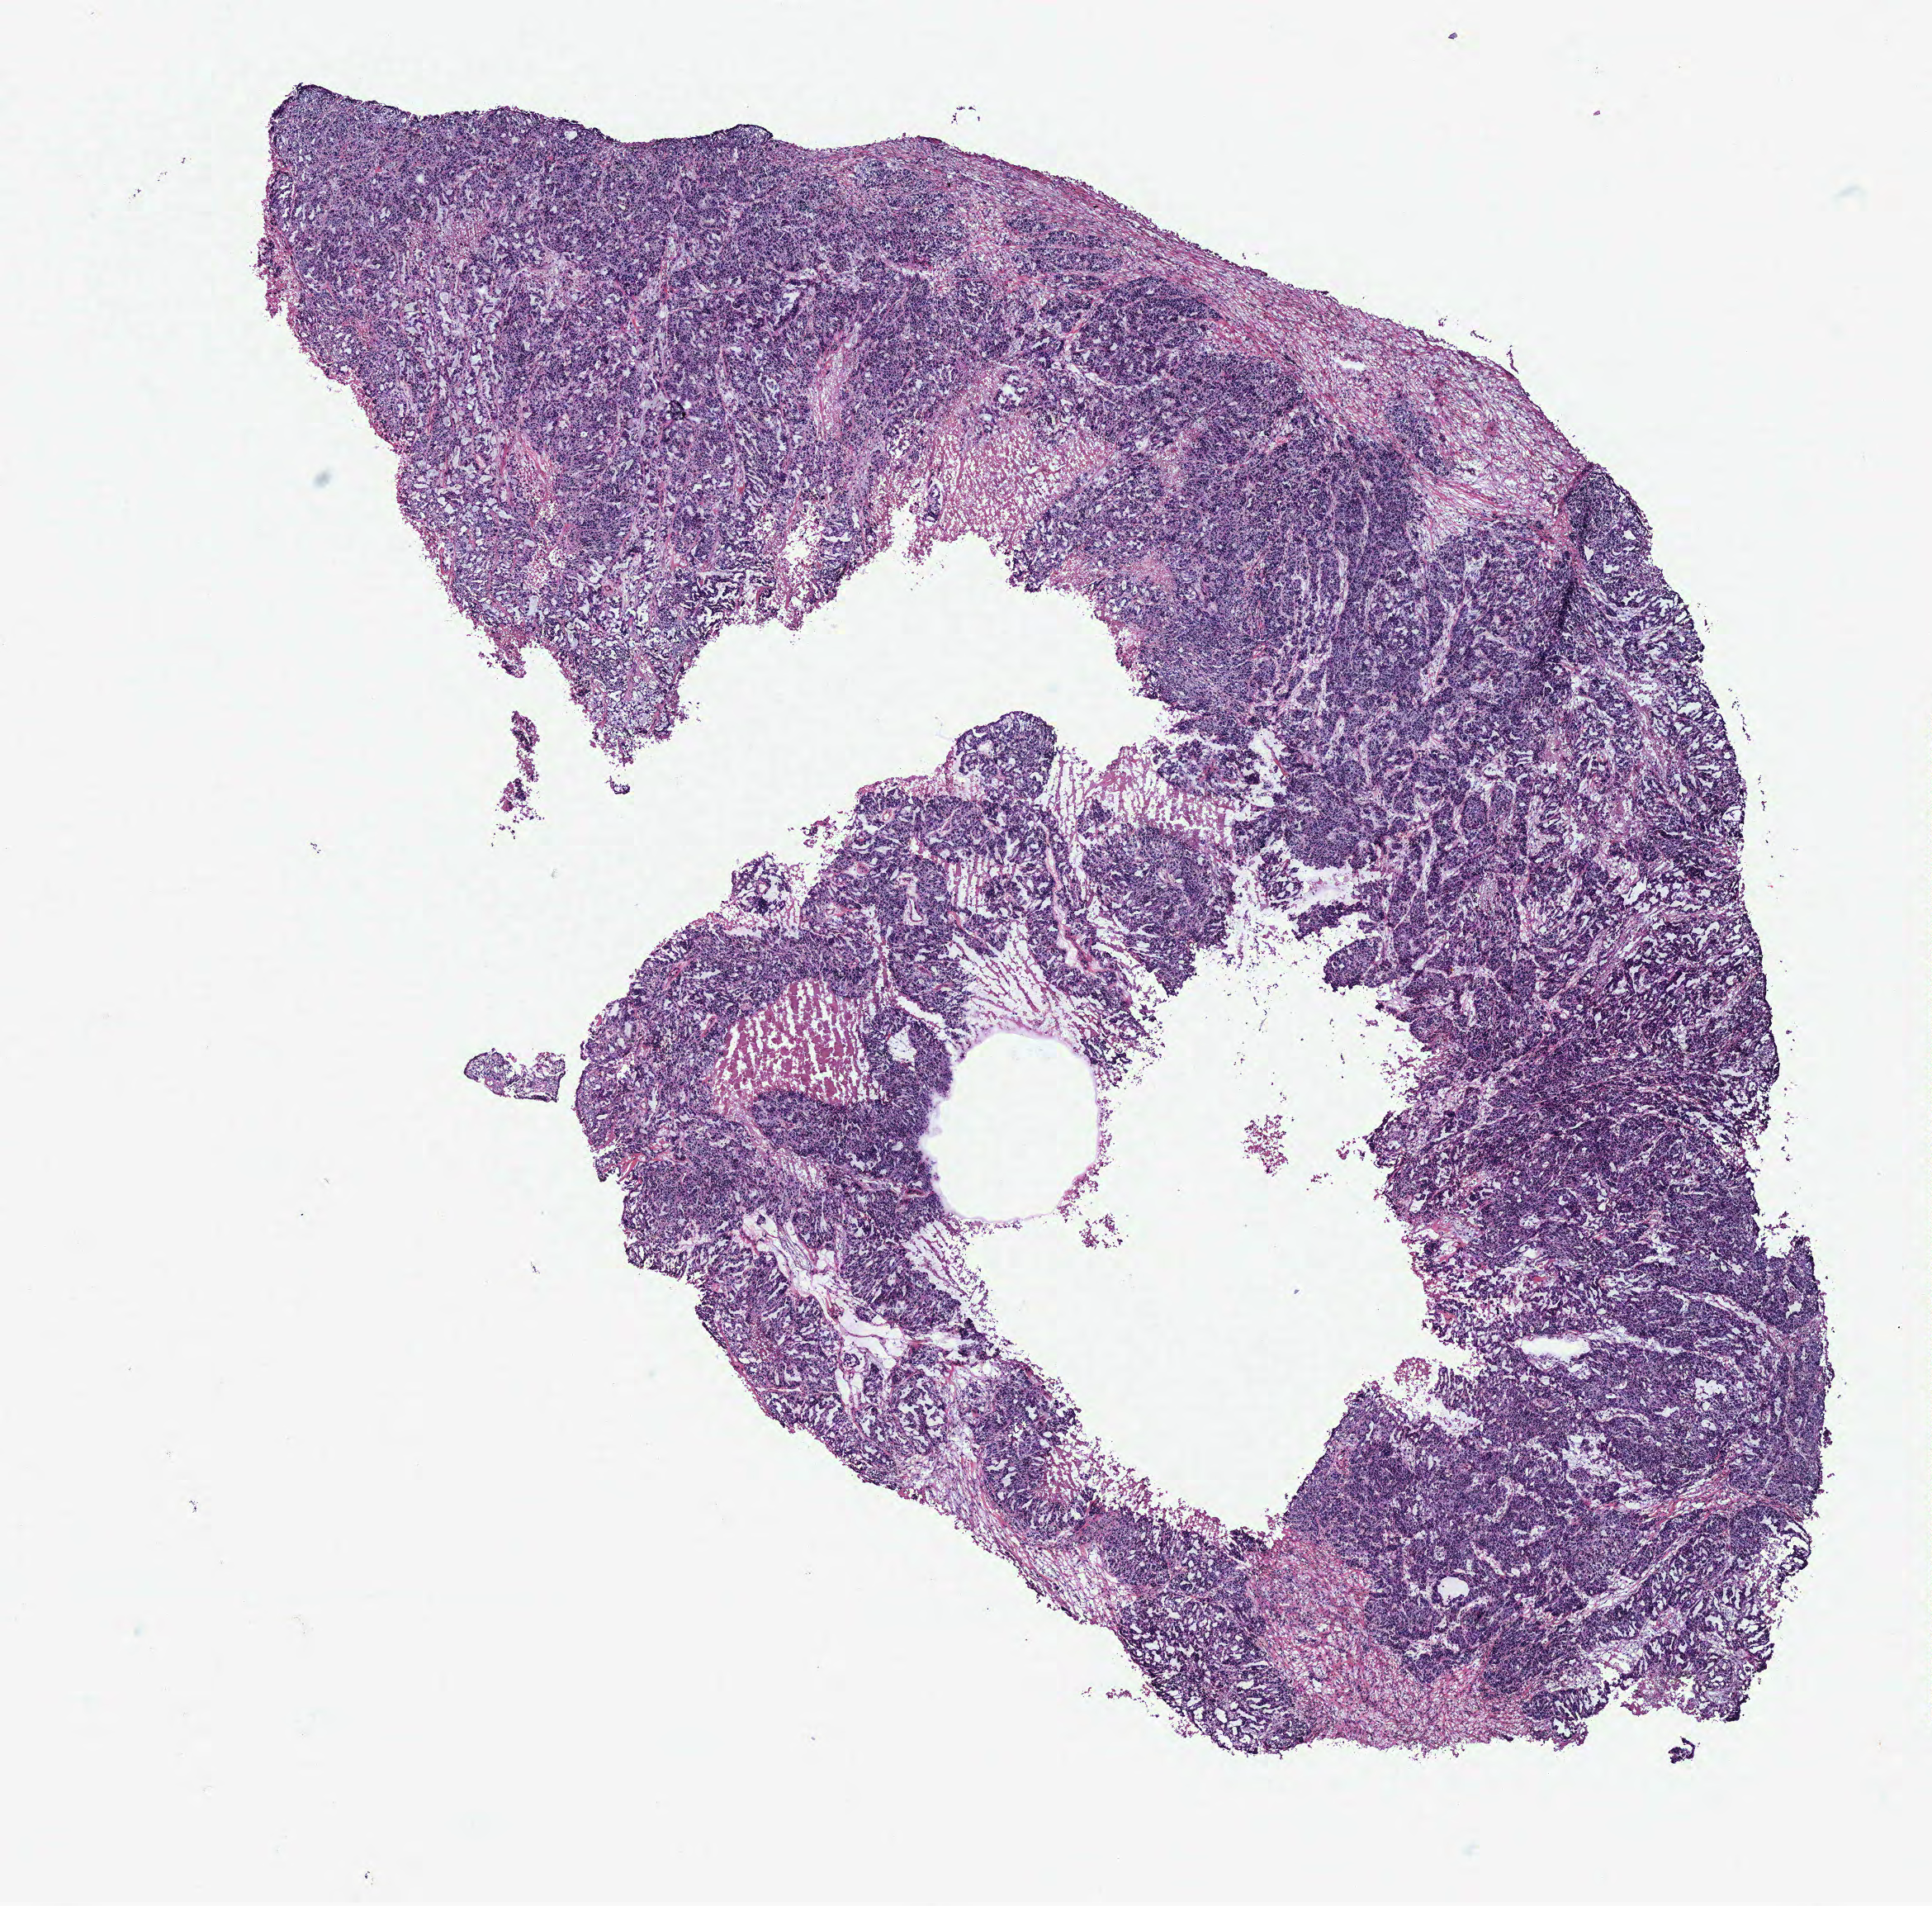
H&E-stained whole-slide image, a low-resolution overview of the entire scanned area, about 9.4 x 9.2 mm (slide scanned at 40x), ovary, tissue type not recorded.
Patient diagnosis (cohort enrolment): ovarian cancer (ovary).